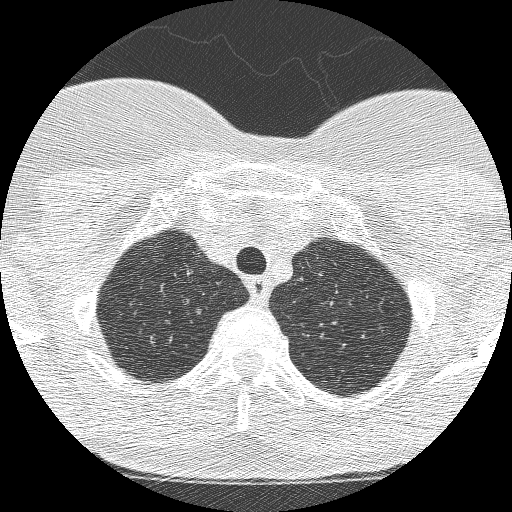
Axial slice from a low-dose chest CT screening exam. Second annual screen. Lung window (W 1500 / L -600 HU). Lung (sharp) reconstruction kernel (BONE). Slice 209 of 250 in the series. Female, age 61 years at enrolment. Current smoker at enrolment.
Lesion marked by an expert reader, bounding box <174,293,217,329> (left, top, right, bottom; pixels). Screening reader's record for this exam (one nodule recorded; not confirmed to be the boxed lesion): non-calcified nodule or mass ≥4 mm, right upper lobe, 11 × 8 mm, poorly defined margins, mixed attenuation, pre-existing on the prior screen: yes; interval growth: yes. Official screen result: positive, change unspecified: nodule(s) >= 4 mm or enlarging nodule(s), mass(es), or other non-specific abnormalities suspicious for lung cancer.